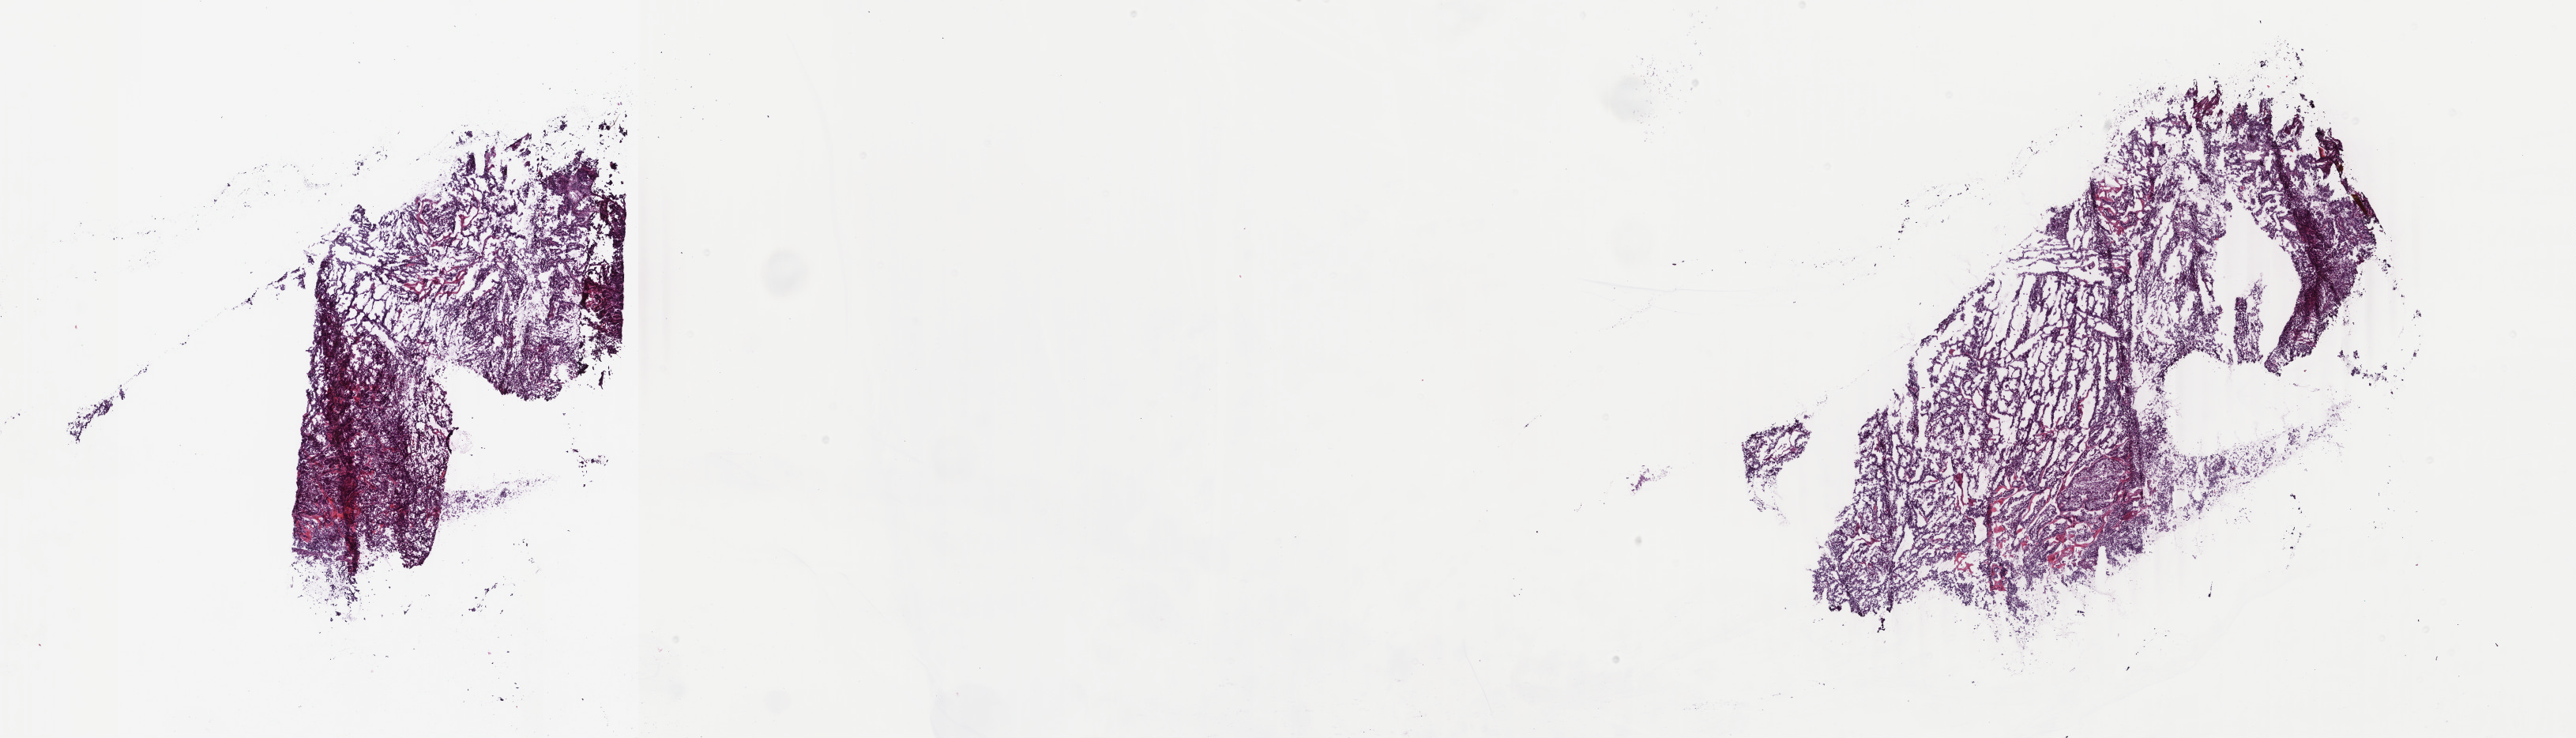
Digitized Hematoxylin and eosin (H&E) stained tissue section (whole slide), low-resolution overview of the scanned area, about 25.9 x 7.4 mm (slide scanned at 40x). Frozen section. Sample: primary tumour, uterus. Female, age 67 years at initial diagnosis. Pathologist review of this section (percent, as recorded): tumour cells 90%, tumour nuclei 95%.
Pathologic diagnosis: Serous cystadenocarcinoma, NOS (endometrium).